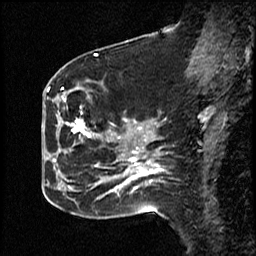
Breast MRI (dynamic contrast-enhanced), one sagittal slice; dynamic contrast-enhanced study with each time point stored as its own series, time point 2 of 4 at this slice position (early post-contrast, ordered by acquisition time); 1.5 T; TE 4.2 ms, TR 18.5 ms; 256 × 256 image matrix, field of view 200 × 200 mm. Patient: female, 44 years. Case-level facts recorded for this patient, not image findings: setting: breast cancer imaged before/during neoadjuvant chemotherapy; receptor status: HR-positive, HER2-negative.
Annotated regions visible in this slice (semi-automatic segmentation, software-assisted and operator-edited):
- analysis volume of interest (the breast-tissue region the enhancement analysis was run in; not a lesion): box from (x=59, y=88) to (x=114, y=206) px
- tumour enhancement mask (voxels above the 100 % enhancement threshold inside the analysis volume of interest): (x=64, y=99)–(x=91, y=138)